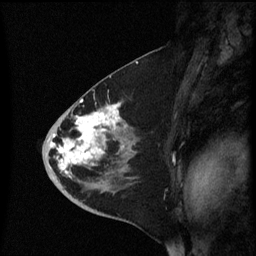
Breast MRI (dynamic contrast-enhanced), one sagittal slice. Position 33 of 60 along the scan axis. Dynamic contrast-enhanced series, image 2 of 3 at this slice position (ordered by acquisition). 1.5 T. TE 4.2 ms, TR 8.4 ms. 2.3 mm slice thickness. 256 × 256 image matrix. Female patient, age 46 years. Case-level facts recorded for this patient, not image findings: setting: breast cancer imaged before/during neoadjuvant chemotherapy; receptor status: HER2-positive.
Annotated regions visible in this slice (semi-automatic segmentation, software-assisted and operator-edited):
- analysis volume of interest (the breast-tissue region the enhancement analysis was run in; not a lesion): bounding box [x1, y1, x2, y2] px = [43, 96, 137, 187]
- tumour enhancement mask (voxels above the 70 % enhancement threshold inside the analysis volume of interest): [51, 104, 126, 175]